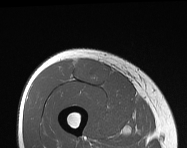
MRI of an extremity soft-tissue mass, one axial slice; slice 53 of 114 in the series (ordered by position); MR volume resampled by the dataset authors to the PET/CT grid (not the native acquisition matrix); 3.27 mm slice thickness; 187 × 148 image matrix, field of view 183 × 145 mm. Male patient. From the clinical record (not read from this slice): histological type: pleiomorphic leiomyosarcoma; grade: intermediate; site of the primary tumour: right thigh.
Structures marked on this image (expert contour drawn on MRI and transferred to this co-registered scan by the dataset authors):
- gross tumour volume including surrounding oedema: bounding box [x1, y1, x2, y2] px = [73, 58, 112, 85]